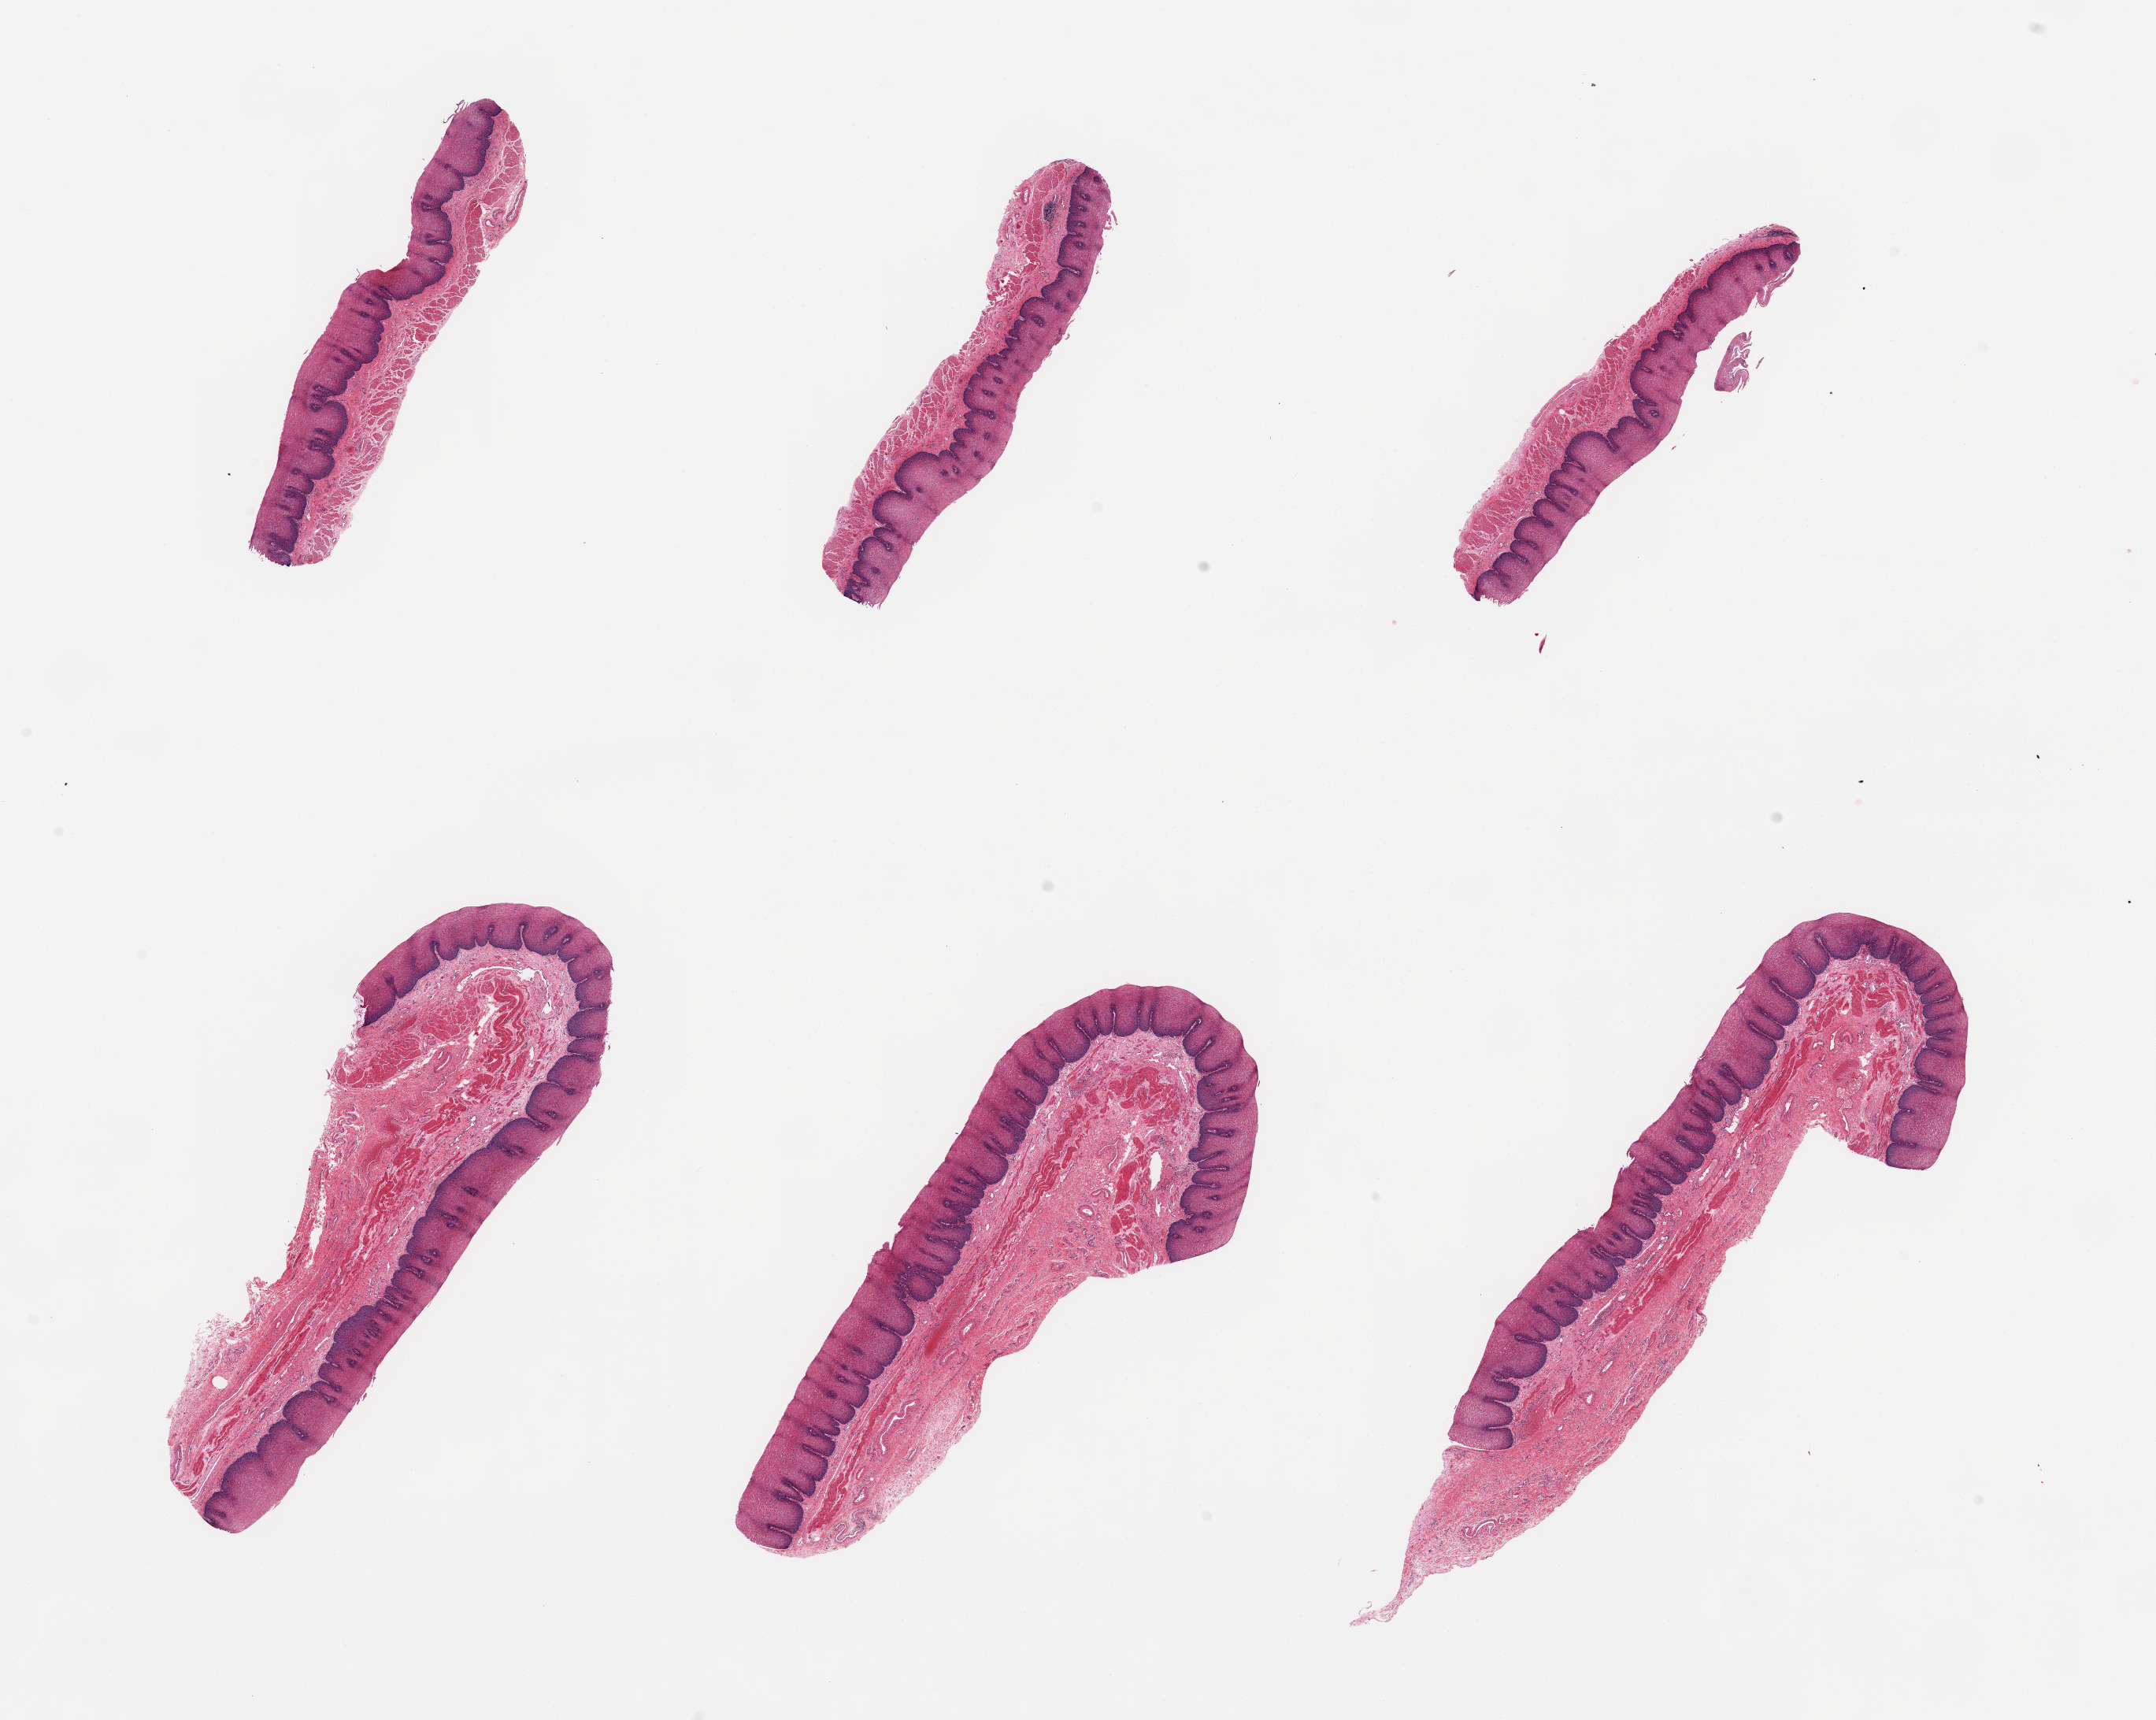
H&E whole-slide image, brightfield — shown as a low-resolution overview of the whole scanned area (about 21.7 x 17.3 mm), PAXgene-fixed paraffin-embedded (PFPE) section, sampled site (target tissue): esophageal mucous membrane, donor tissue sample. Donor sex: male.
Pathologist's review note for this sample: 6 pieces, squamous mucosa is ~0.5mm, ~50-60% thickness.